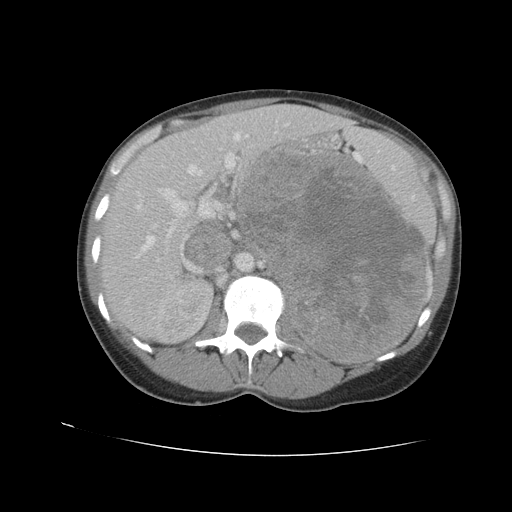
Contrast-enhanced abdominal CT, one axial slice; reconstruction kernel STANDARD; soft-tissue window (W 400 / L 40 HU); 5 mm slice thickness; 512 × 512 image matrix, field of view 360 × 360 mm. Female patient. From the clinical record (not read from this slice): diagnosis: adrenocortical carcinoma; tumour side: left adrenal; tumour size at pathology: 18 cm; Ki-67 index: 11 %; stage (as recorded): 3.
Structures marked on this image (semi-automatically segmented with operator editing):
- mass: bounding box [x1, y1, x2, y2] px = [246, 151, 428, 358]